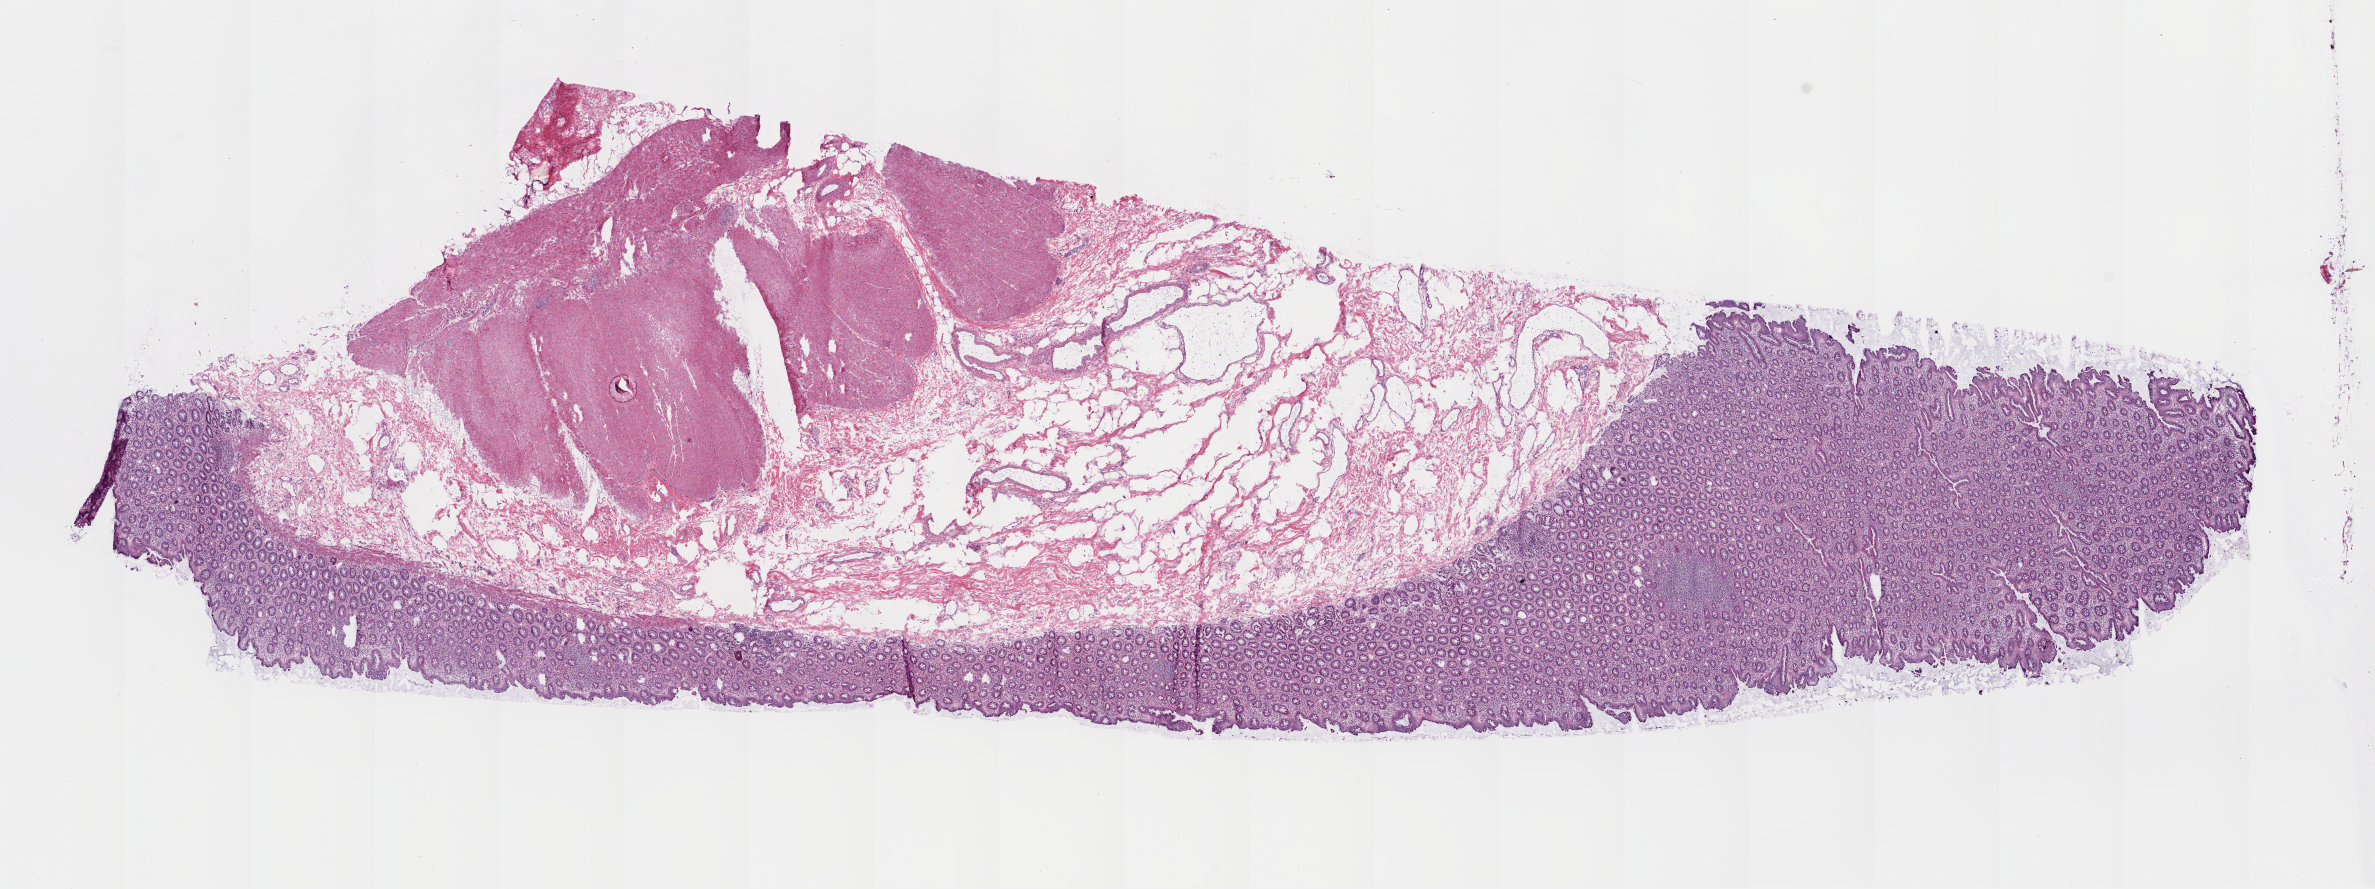
Hematoxylin and eosin (H&E) stained whole-slide image, whole scanned area (about 19.1 x 7.1 mm) shown as a low-resolution overview, frozen section from the top of the tissue portion, solid tissue normal (non-tumour tissue) sample from the rectum. Female, age 54 years at initial diagnosis.
This section: solid tissue normal (non-tumour) sample from the same patient. Patient diagnosis: Adenocarcinoma, NOS.